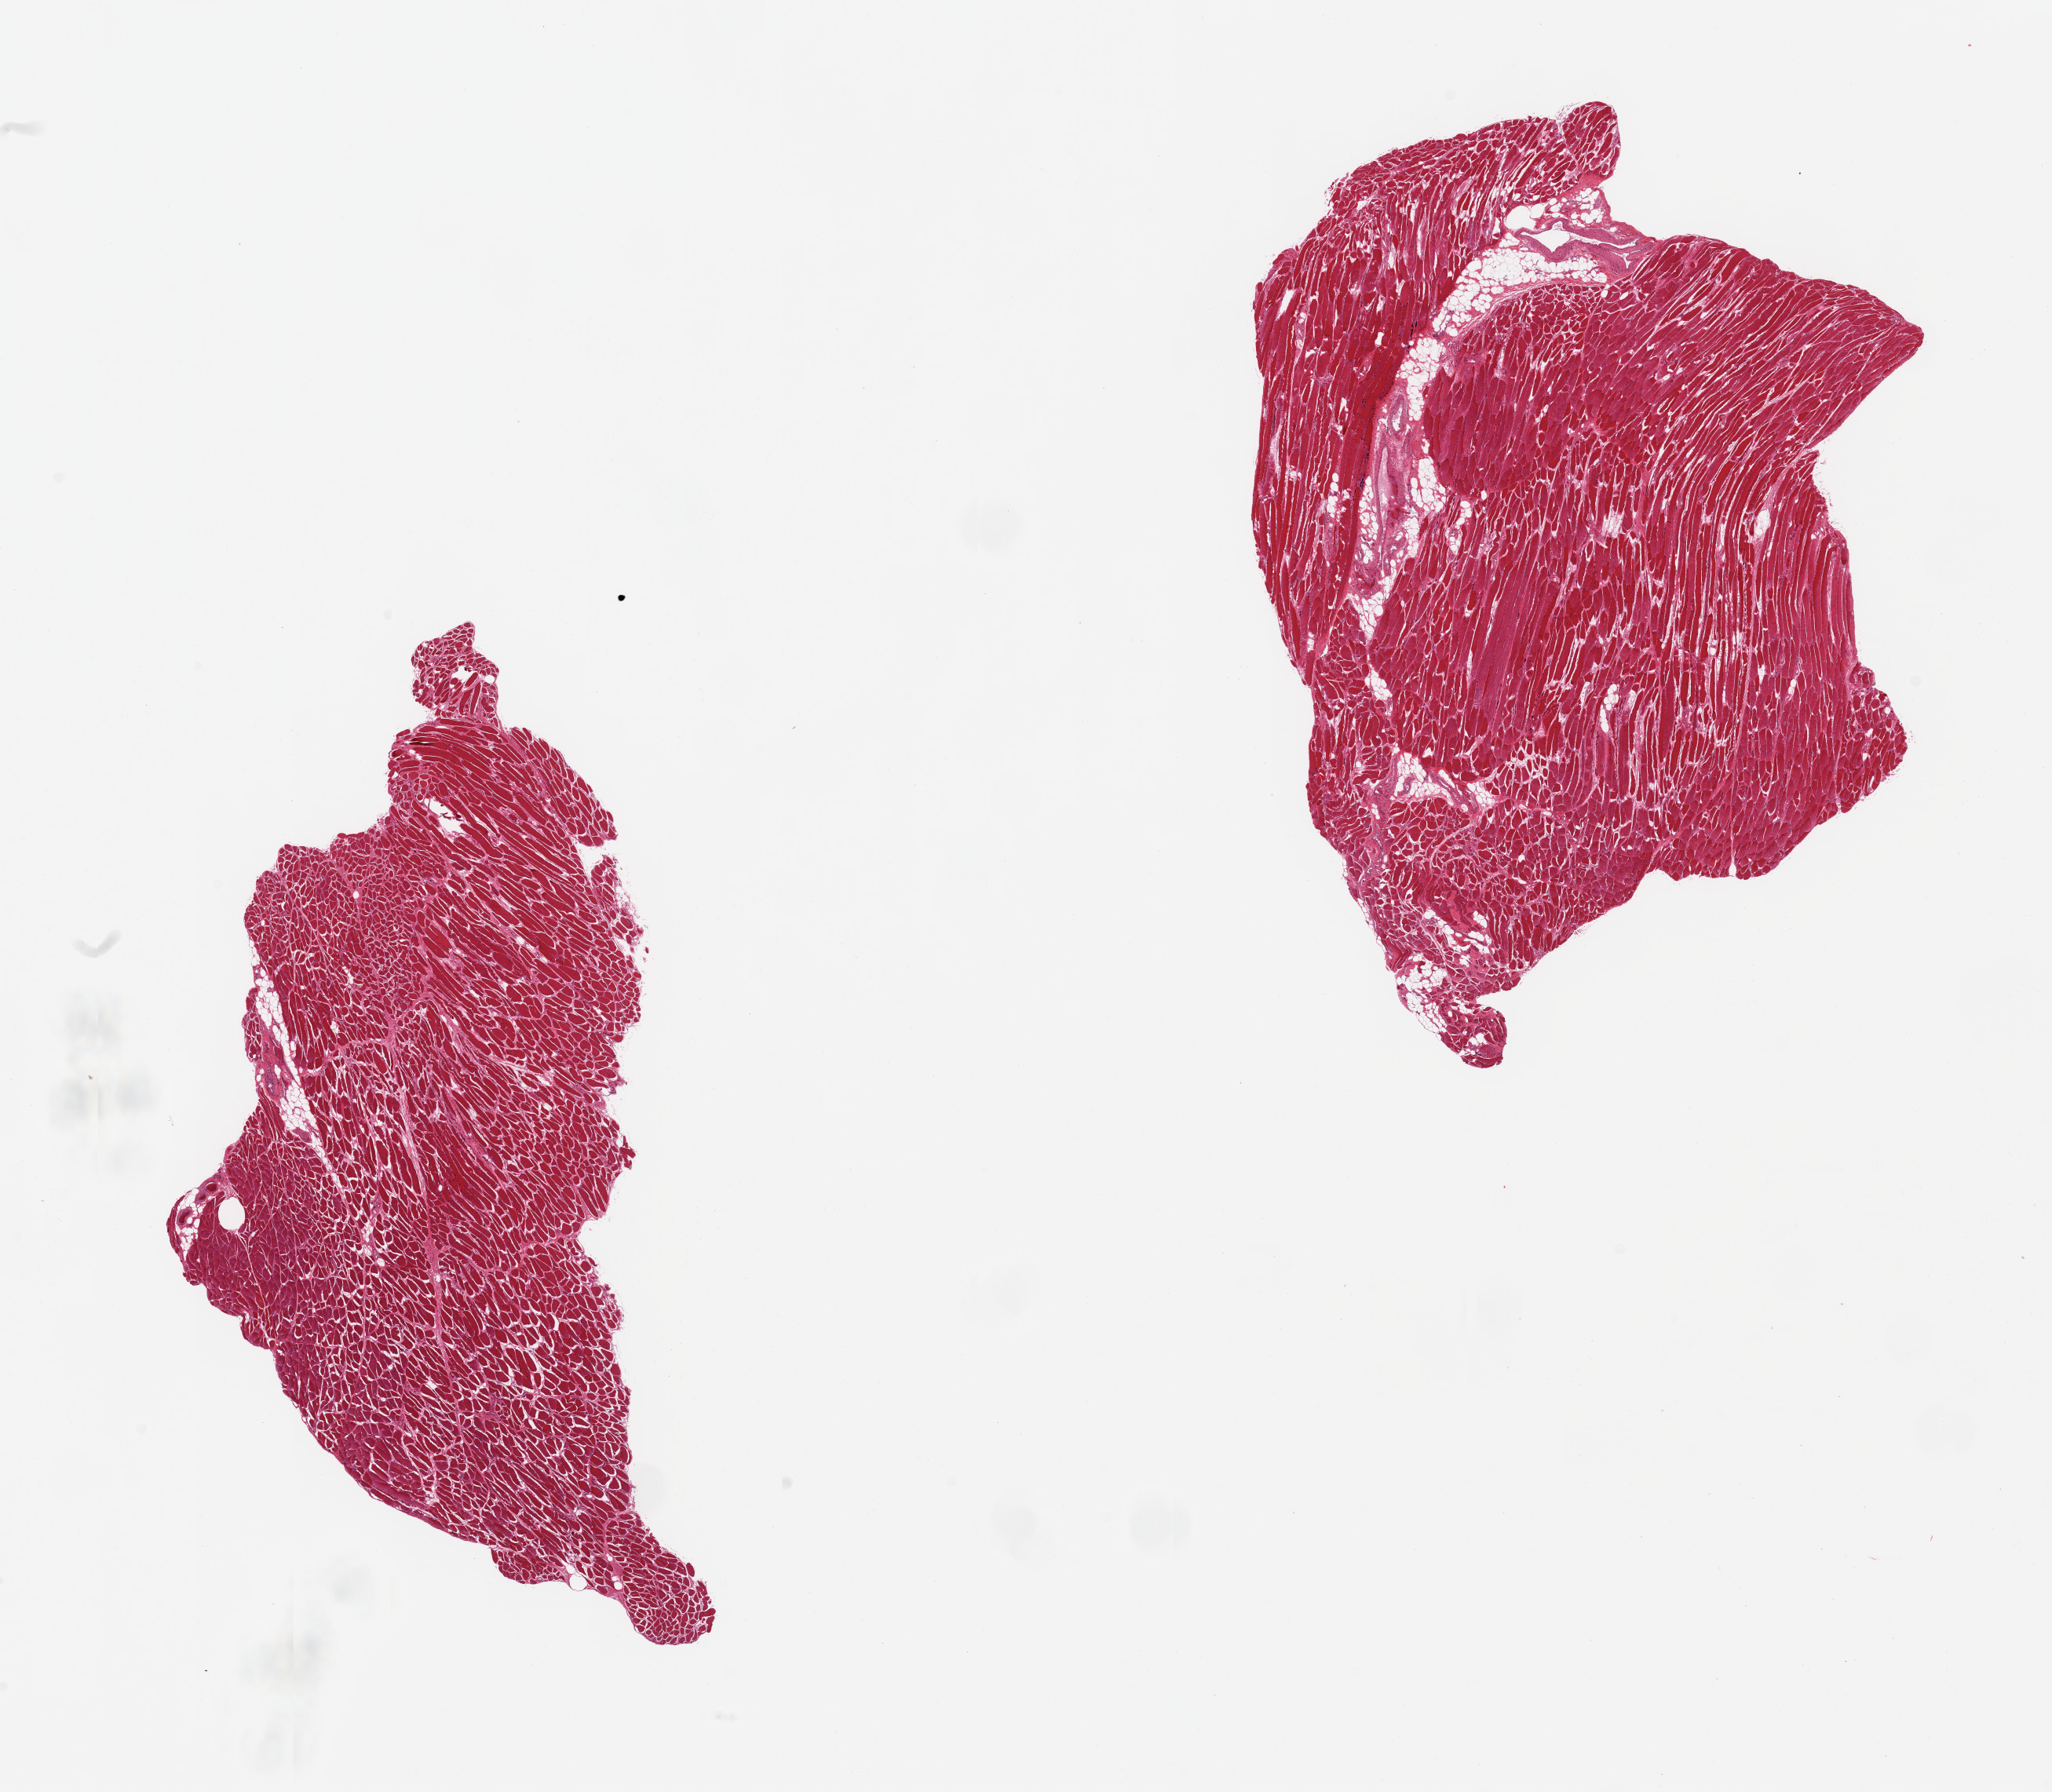
Whole-slide image, hematoxylin and eosin (H&E) stain — whole scanned area (about 20.7 x 18.1 mm) shown as a low-resolution overview; PAXgene-fixed paraffin-embedded (PFPE) section; sampled site (target tissue): skeletal muscle; donor tissue sample. Male donor.
Pathologist's review note for this sample: 2 pieces; one includes ~5% internal fat/vessels, nuclear internalization and some atrophy.